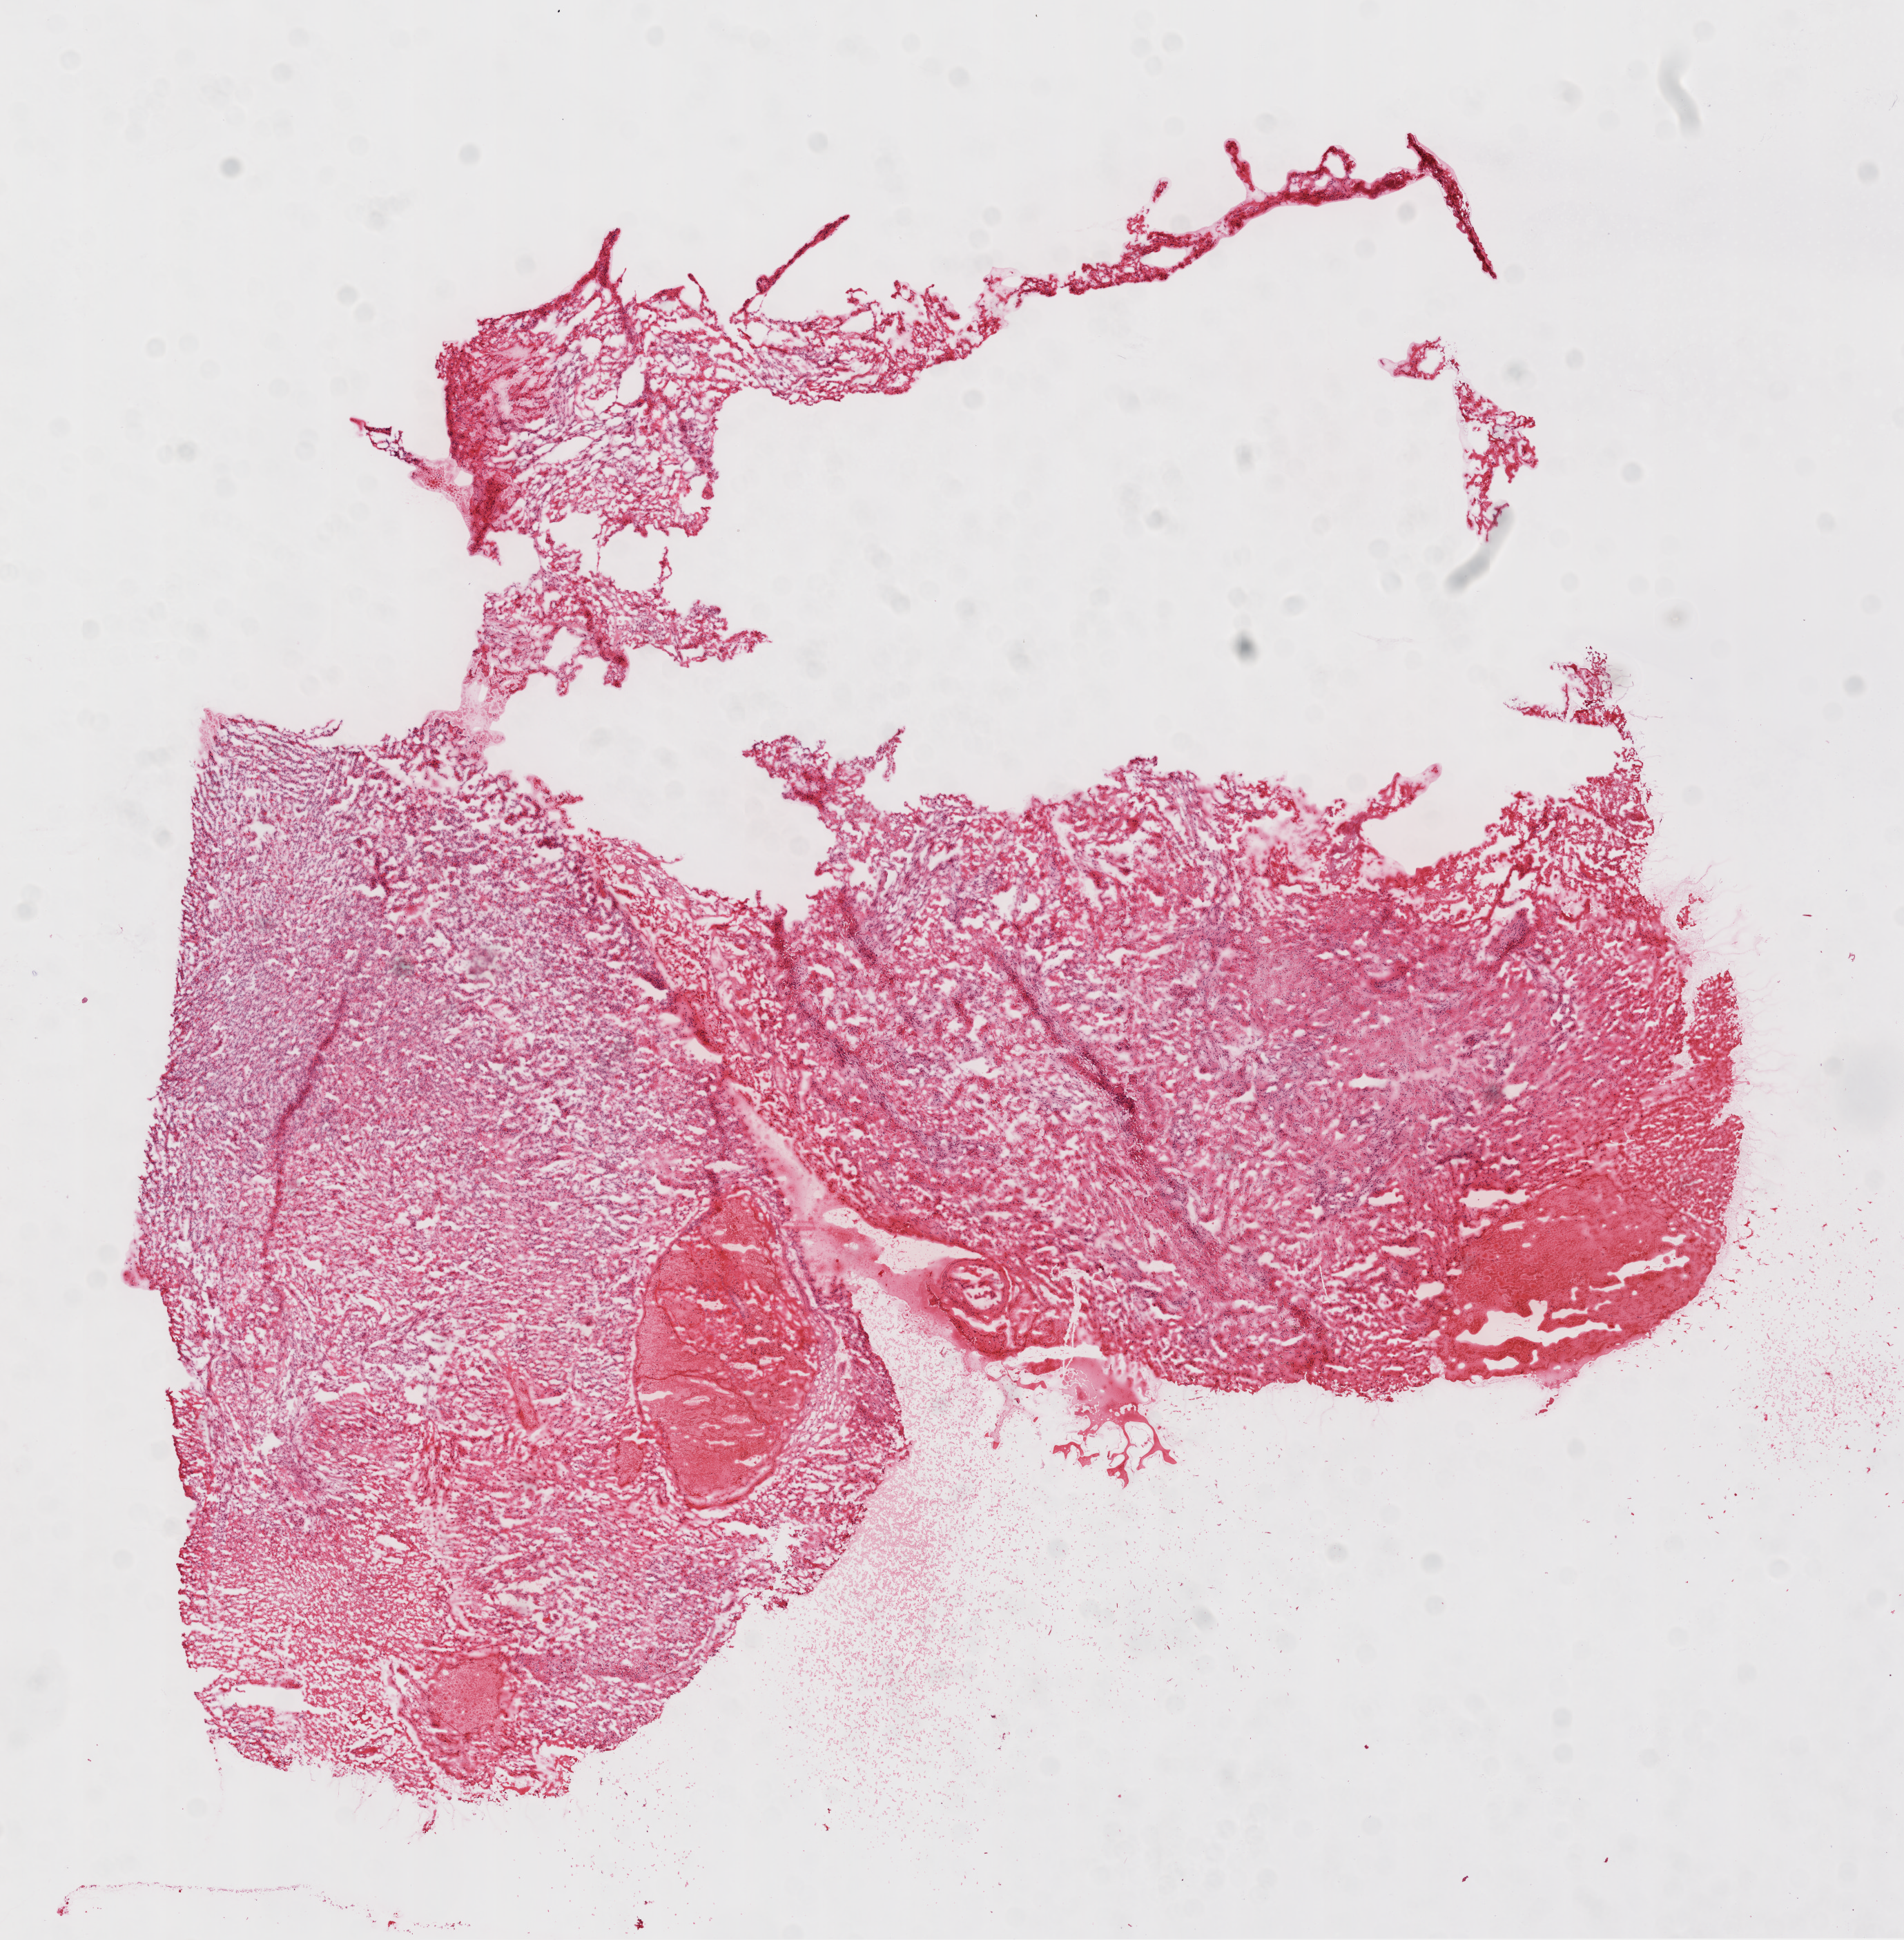
Whole-slide histology image, Hematoxylin and eosin (H&E) stained, shown as a low-resolution overview of the whole scanned area (about 11.1 x 11.3 mm). Frozen section from the top of the tissue portion. Sample: primary tumour, brain. Patient: female, age at initial diagnosis 75 years. Pathologist review of this section (percent, as recorded): tumour cells 90%, tumour nuclei 100%, normal cells 0%, stromal cells 0%, necrosis 10%.
* pathologic diagnosis: Glioblastoma